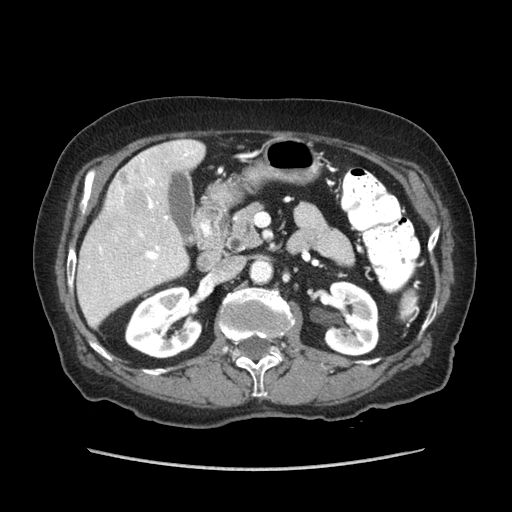
Contrast-enhanced abdominal CT (liver protocol), one axial slice. Slice 32 of 89 in the series (ordered by position). Reconstruction kernel STANDARD. 140 kVp. Soft-tissue window (W 400 / L 40 HU). 2.5 mm slice thickness. 512 × 512 image matrix, field of view 360 × 360 mm. From the clinical record (not read from this slice): diagnosis: hepatocellular carcinoma (patient treated with transarterial chemoembolisation; whether this scan precedes or follows treatment is not stated here); TNM stage (as recorded): Stage-IIIA; Child-Pugh class: A; tumour differentiation: well differentiated; tumour size: 11 cm.
Annotated regions visible in this slice (semi-automatic segmentation, software-assisted and operator-edited):
- liver parenchyma outside the tumour (the mass and vessels are separate outlines, so this box may not span the whole liver): bounding box [x1, y1, x2, y2] px = [78, 140, 204, 327]
- mass: [103, 158, 148, 222]
- liver vessels: [99, 148, 194, 267]